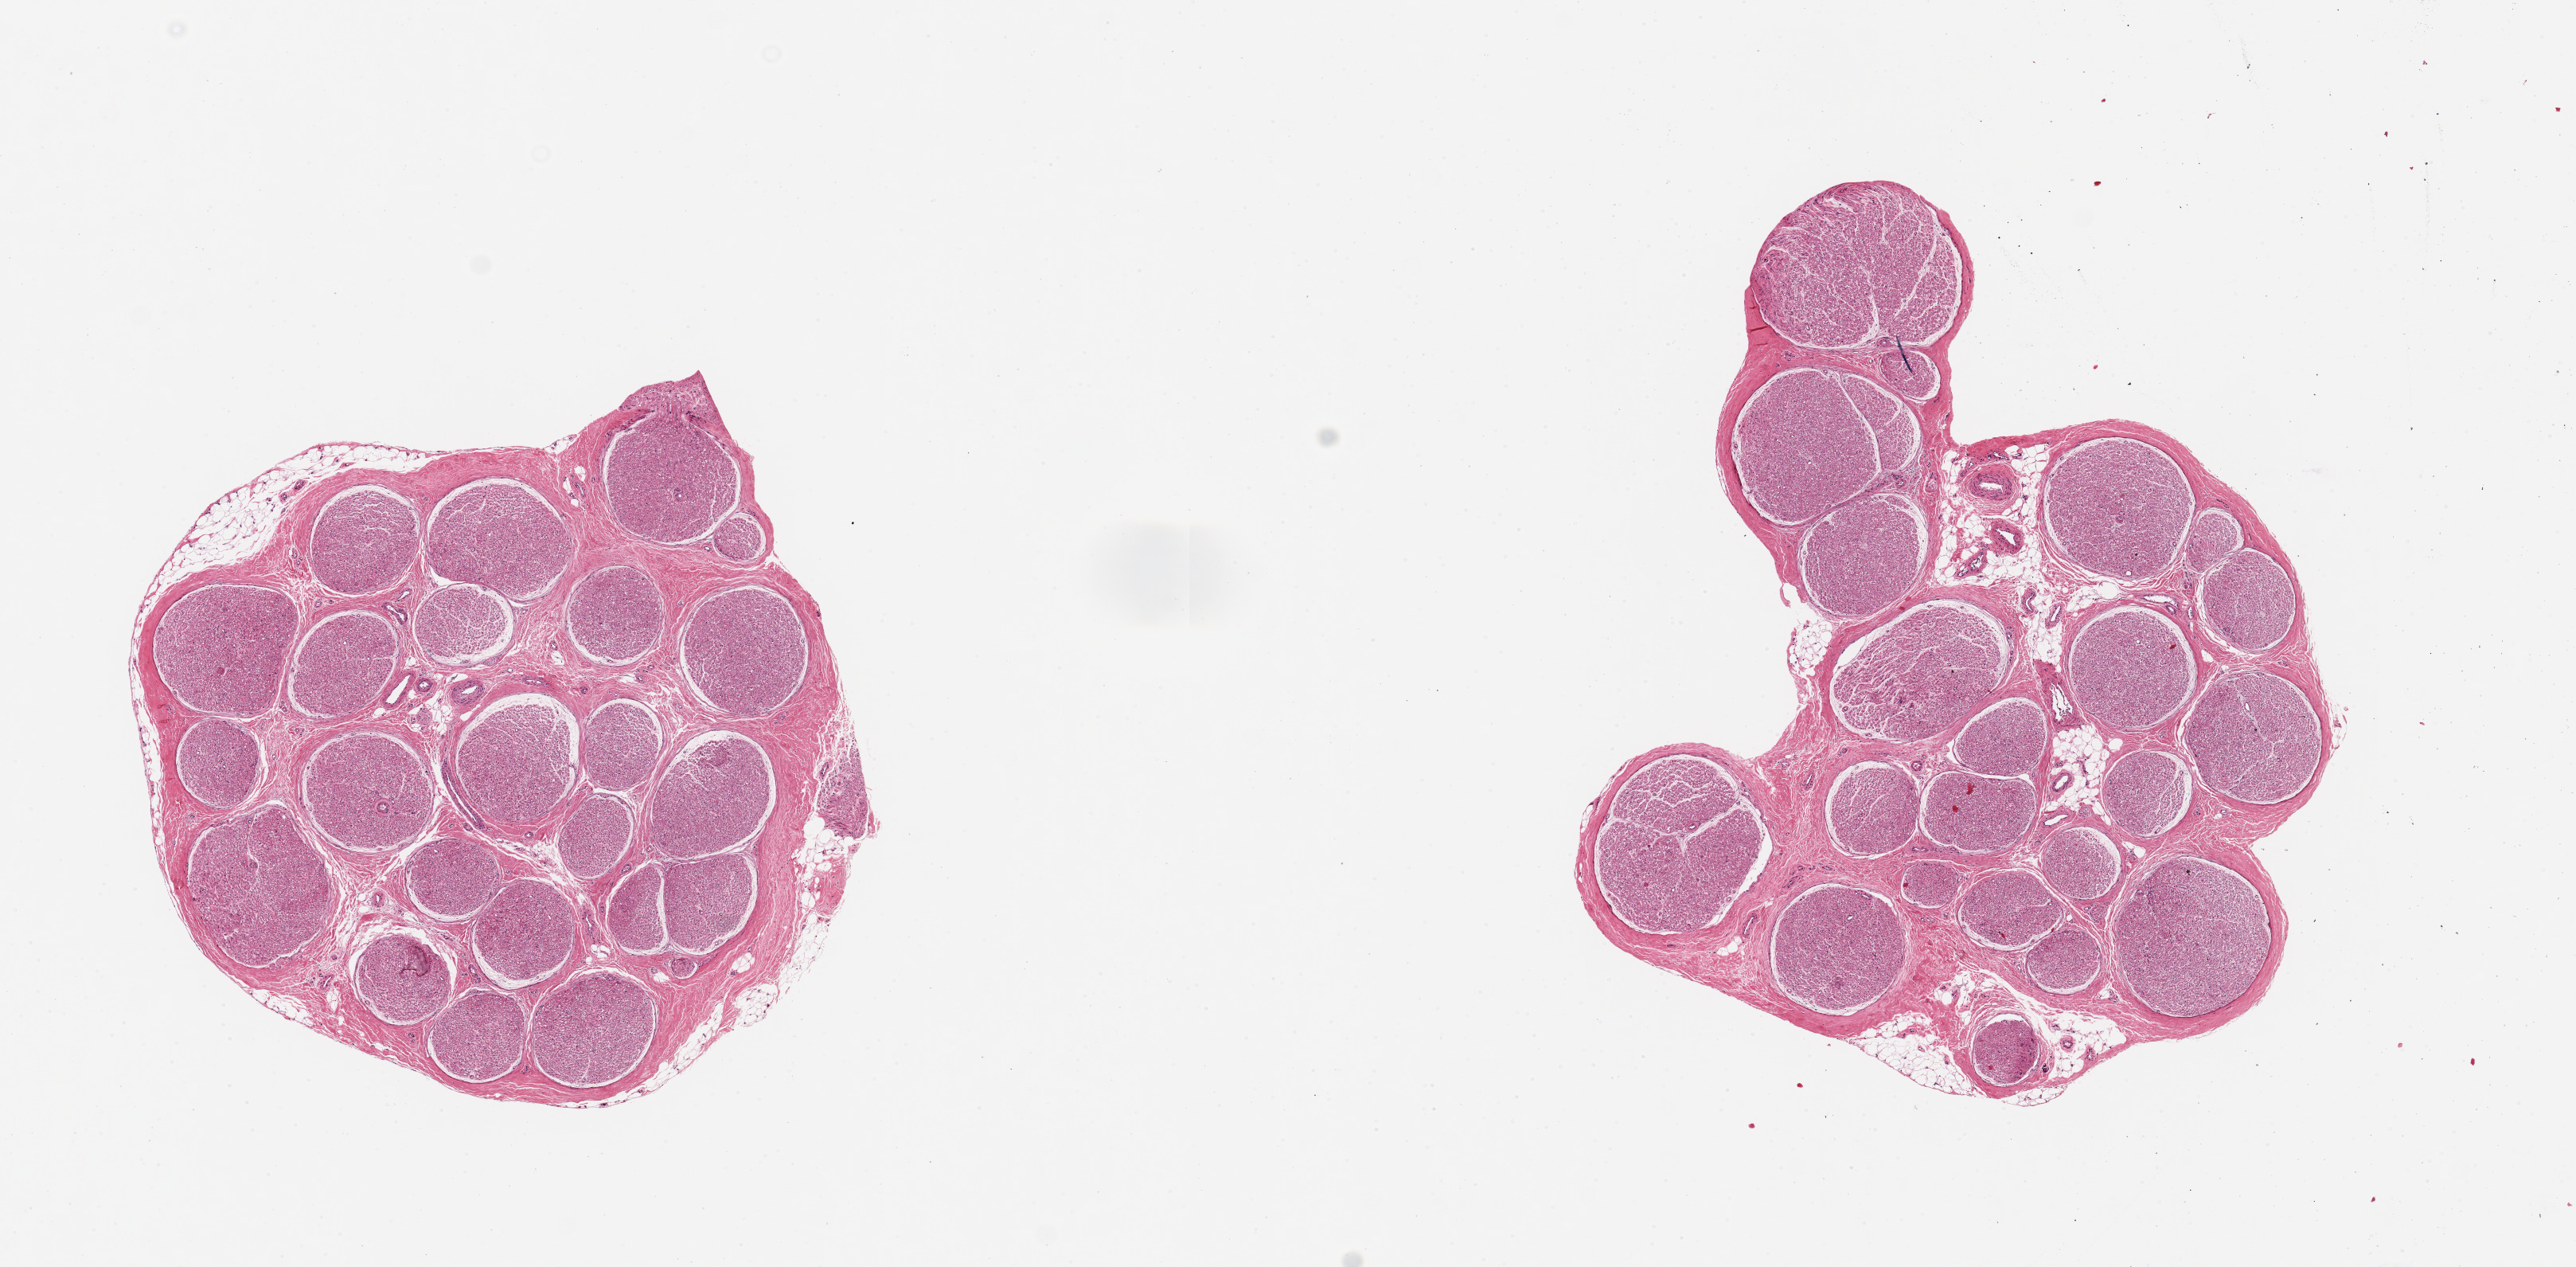
H&E whole-slide image, whole scanned area (about 12.8 x 6.3 mm, acquisition: 20x scan) shown as a low-resolution overview; PAXgene-fixed paraffin-embedded (PFPE) section; sampled site (target tissue): tibial nerve; donor tissue sample.
Review note (as recorded): 2 aliquots, ~4mm d.